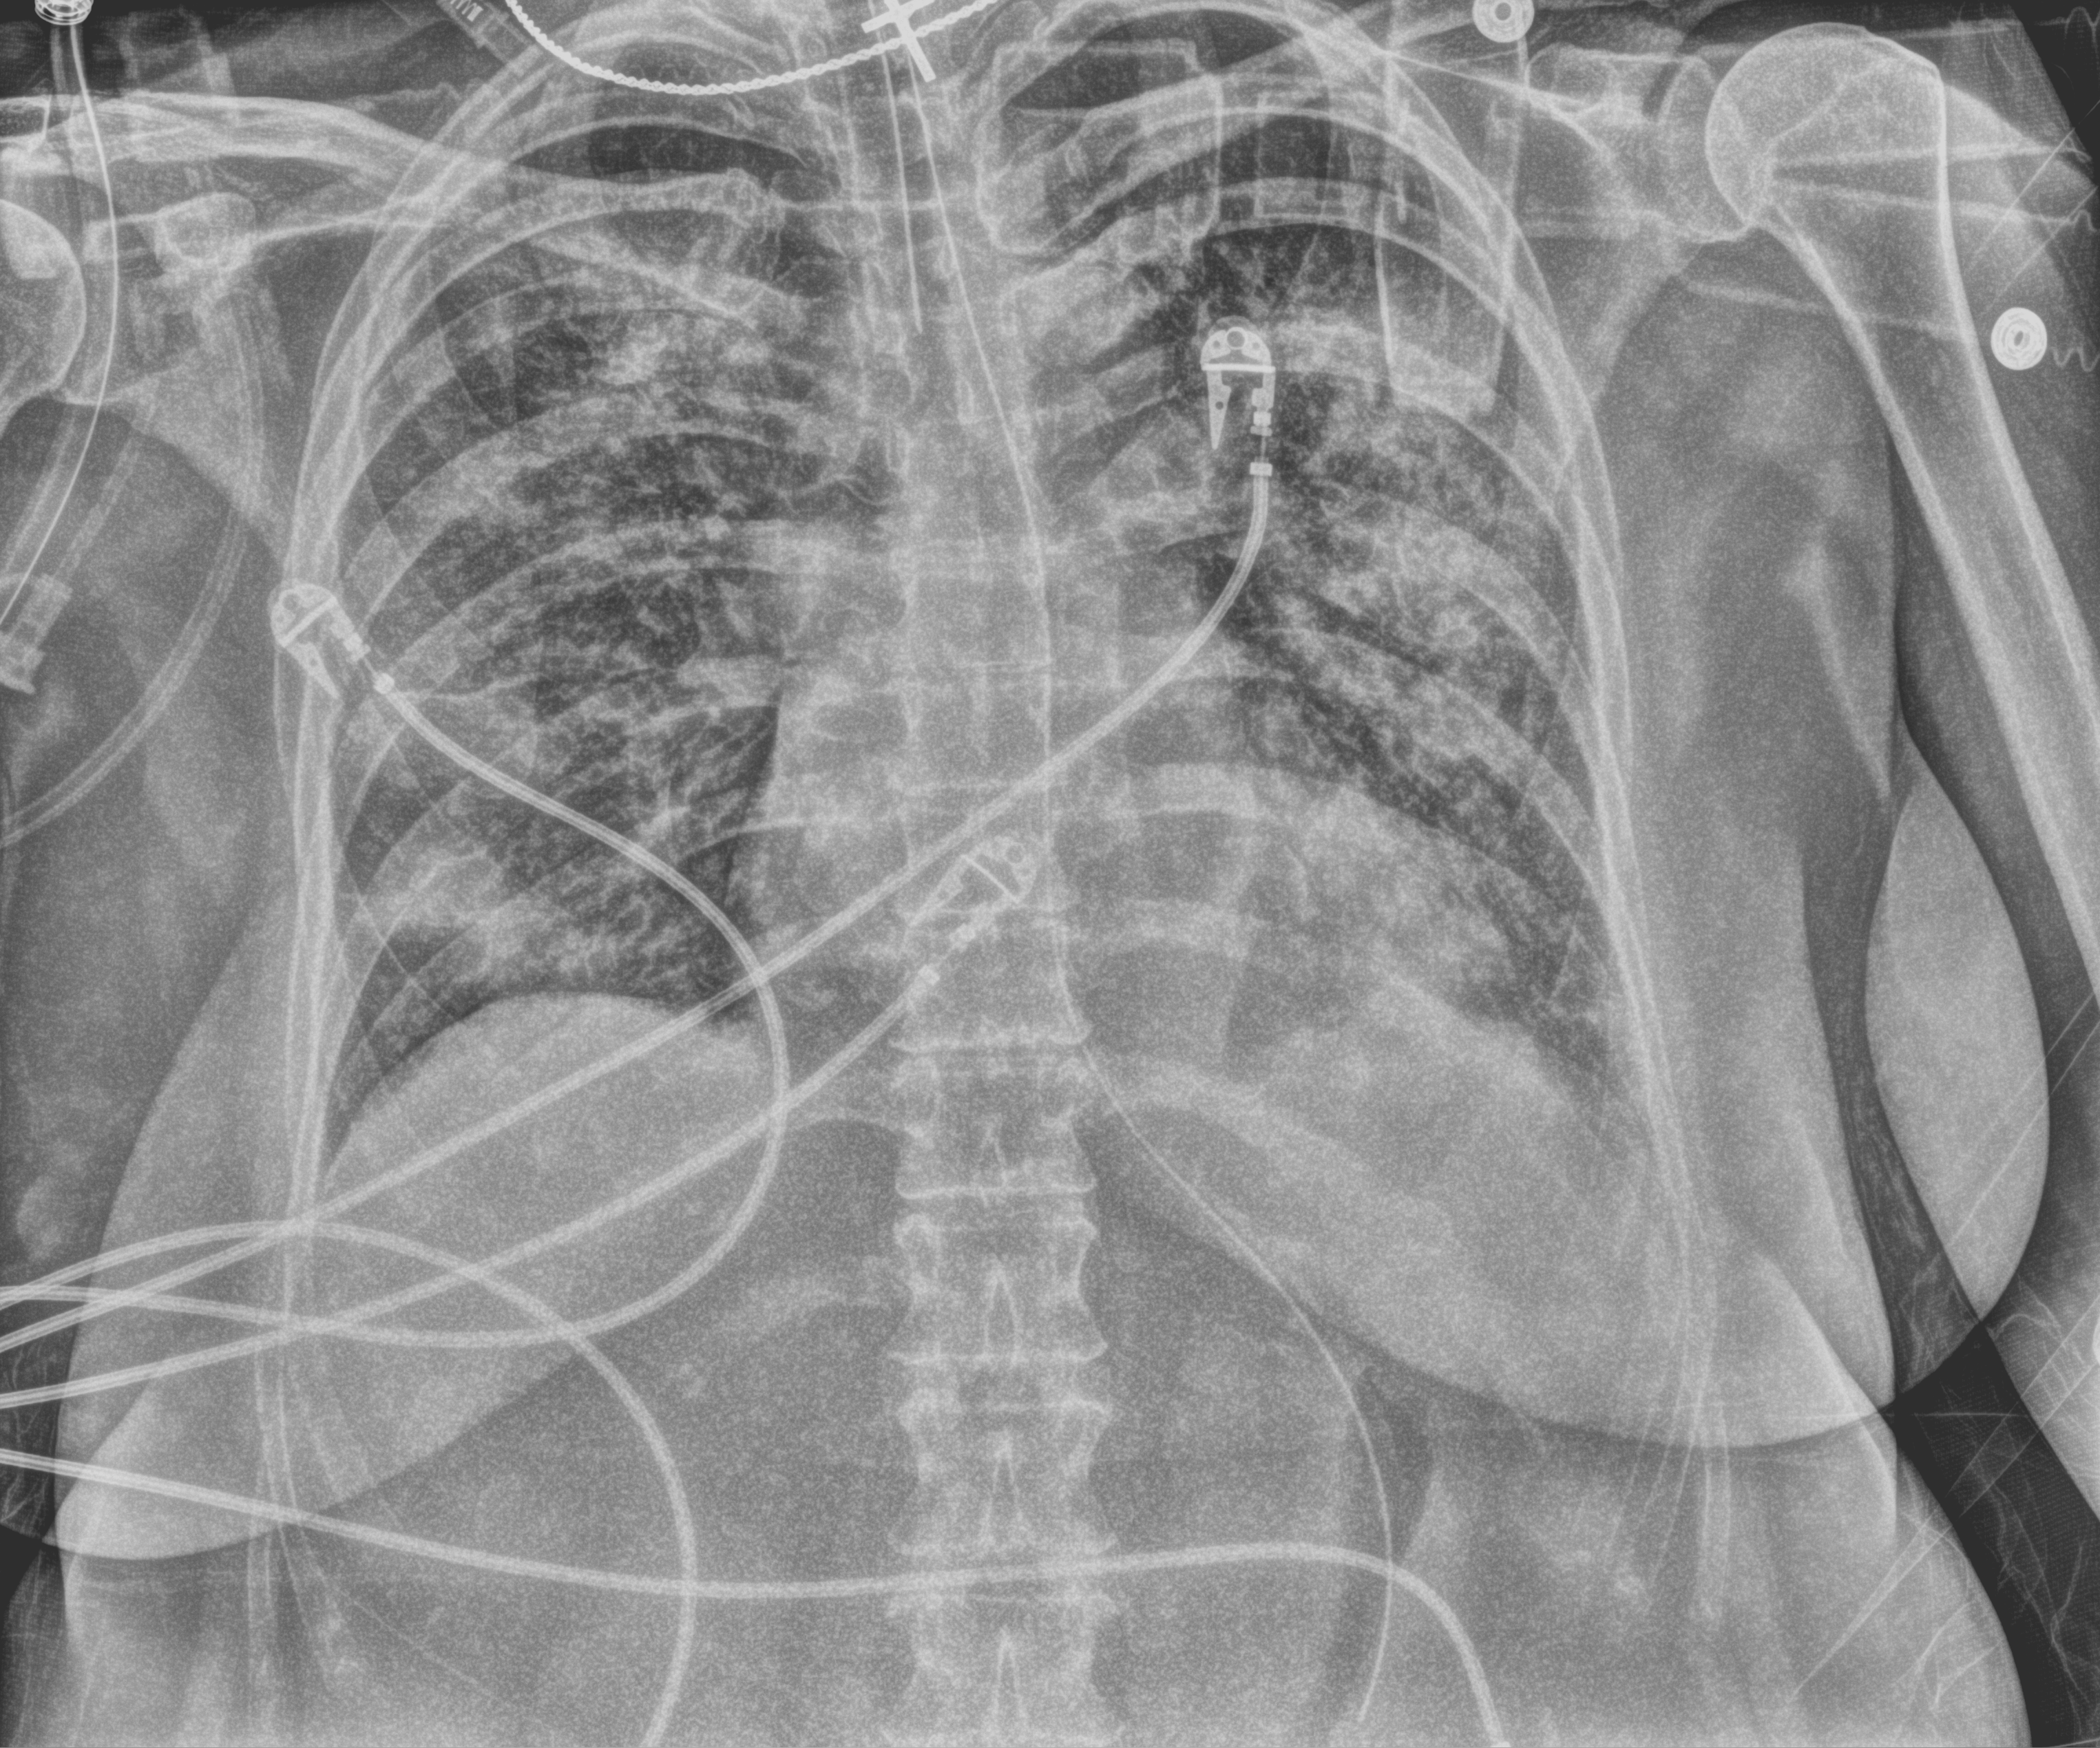
Portable chest radiograph, anteroposterior (AP) projection. Female patient hospitalised with COVID-19, age 18–59 years.
Hospital-stay facts (about this admission, not read from this image; timing relative to this image not recorded):
- admitted to intensive care during this hospital stay: yes
- diabetes (admission record): no